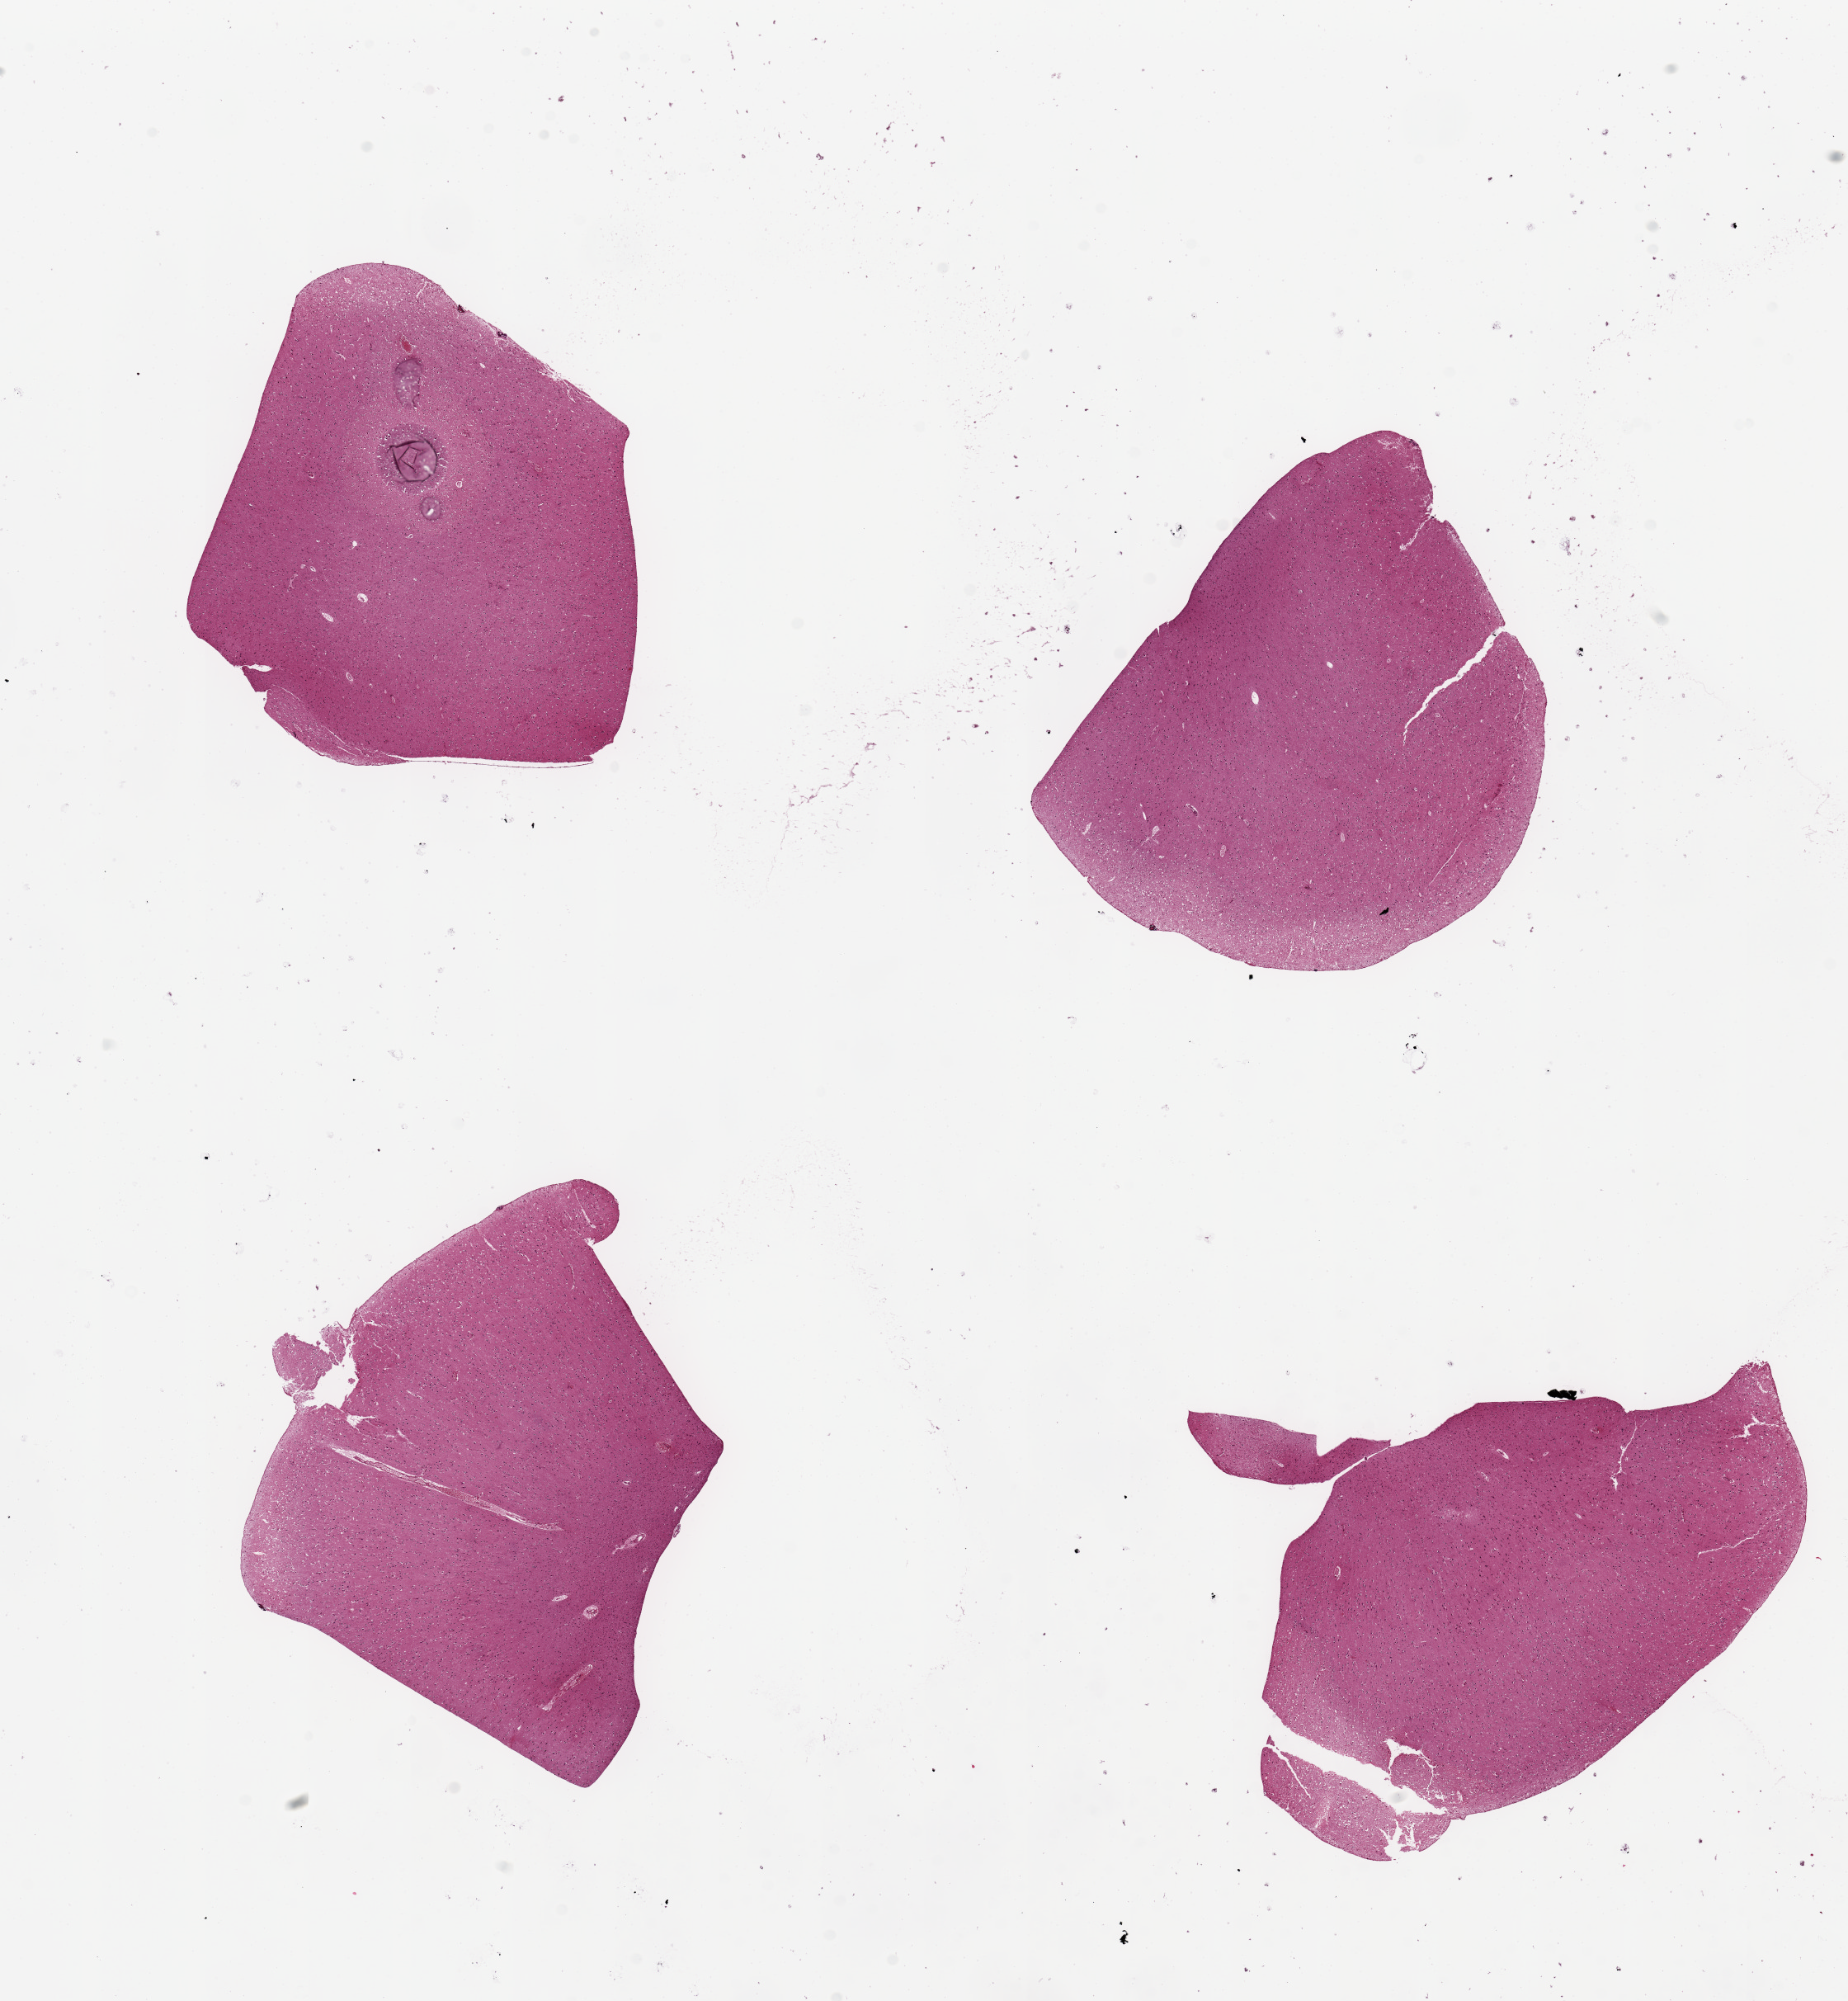
Digitized hematoxylin and eosin (H&E)-stained section — shown as a low-resolution overview of the whole scanned area (about 17.7 x 19.2 mm, slide scanned at 20x); PAXgene-fixed paraffin-embedded (PFPE) section; section of cerebral cortex (target tissue); tissue donor sample.
Pathologist's review note for this sample: 4 pieces. up to 6x6mm.